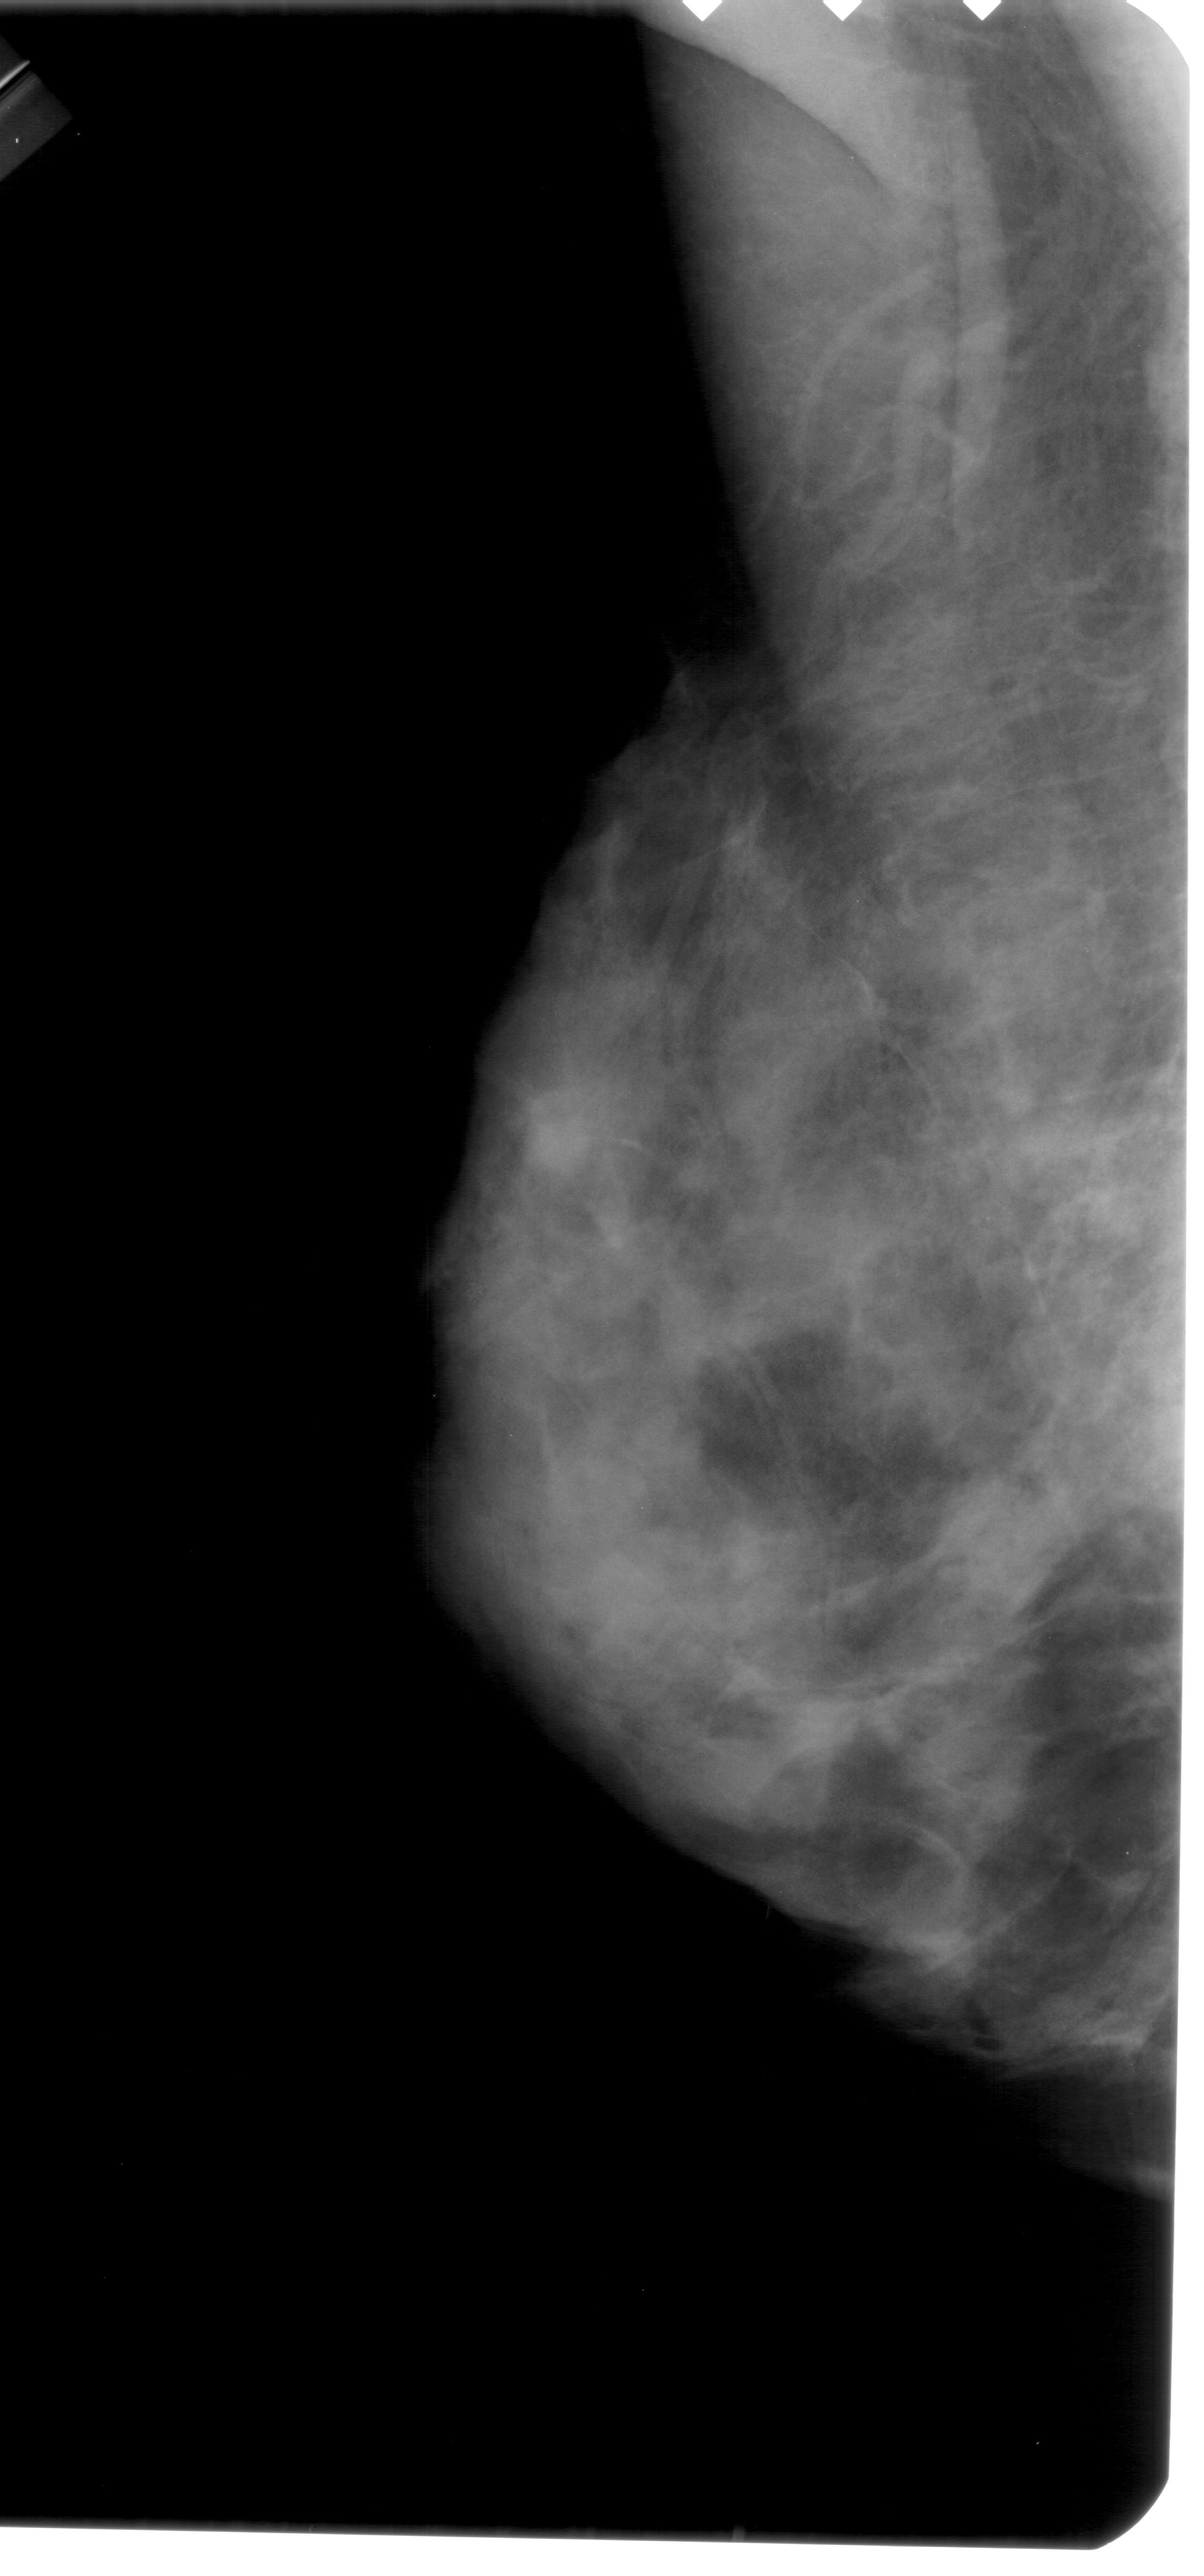
Digitized screen-film mammogram, left breast, mediolateral oblique (MLO) view, breast composition: extremely dense (BI-RADS density category 4 of 4).
Marked findings (only marked abnormalities are described; nothing is implied about the rest of the image): calcifications, morphology pleomorphic, distribution clustered; BI-RADS assessment category 4; subtlety rating 2 on a 1 (subtle) to 5 (obvious) scale; pathology result (as recorded, not read from the image): benign.